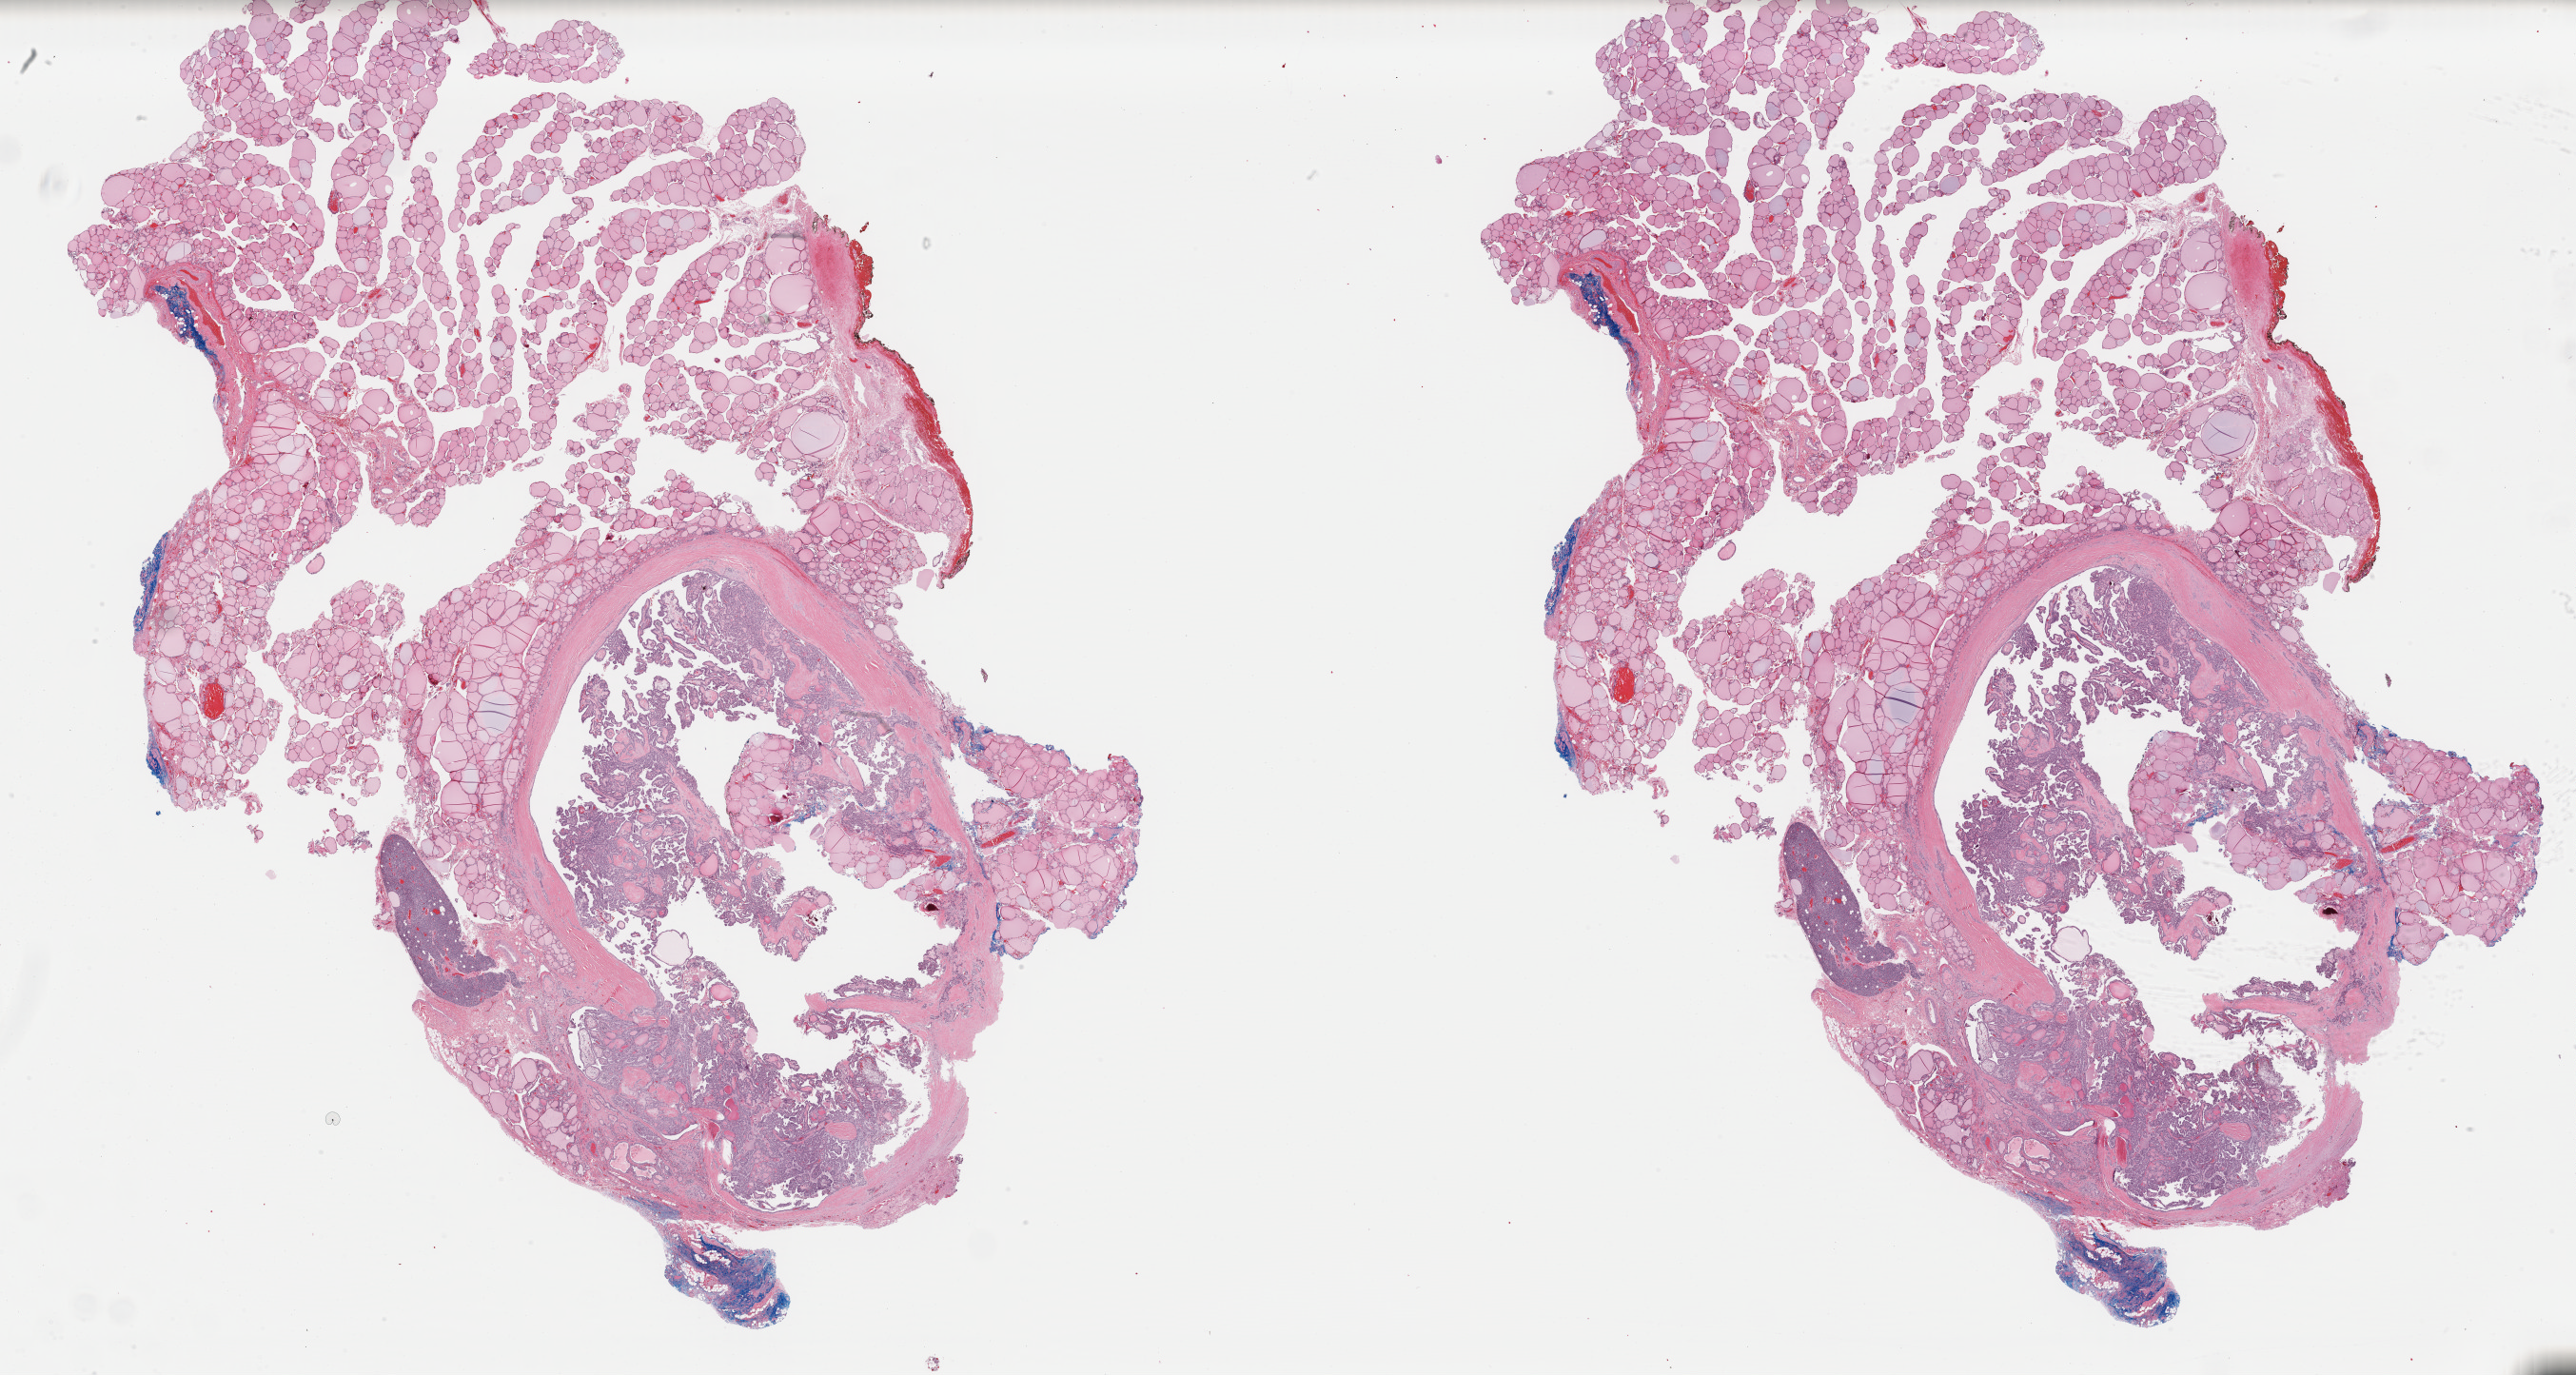
Whole-slide histology image, H&E — shown as a low-resolution overview of the whole scanned area (about 42.7 x 22.8 mm), formalin-fixed paraffin-embedded (FFPE) diagnostic section, thyroid, primary tumour sample. Patient: female, age at initial diagnosis 34 years.
Laterality: left. AJCC pathologic stage: I (7th edition). Lymph nodes positive (case pathology): 13 of 25 examined. Histologic diagnosis: Papillary carcinoma, columnar cell.